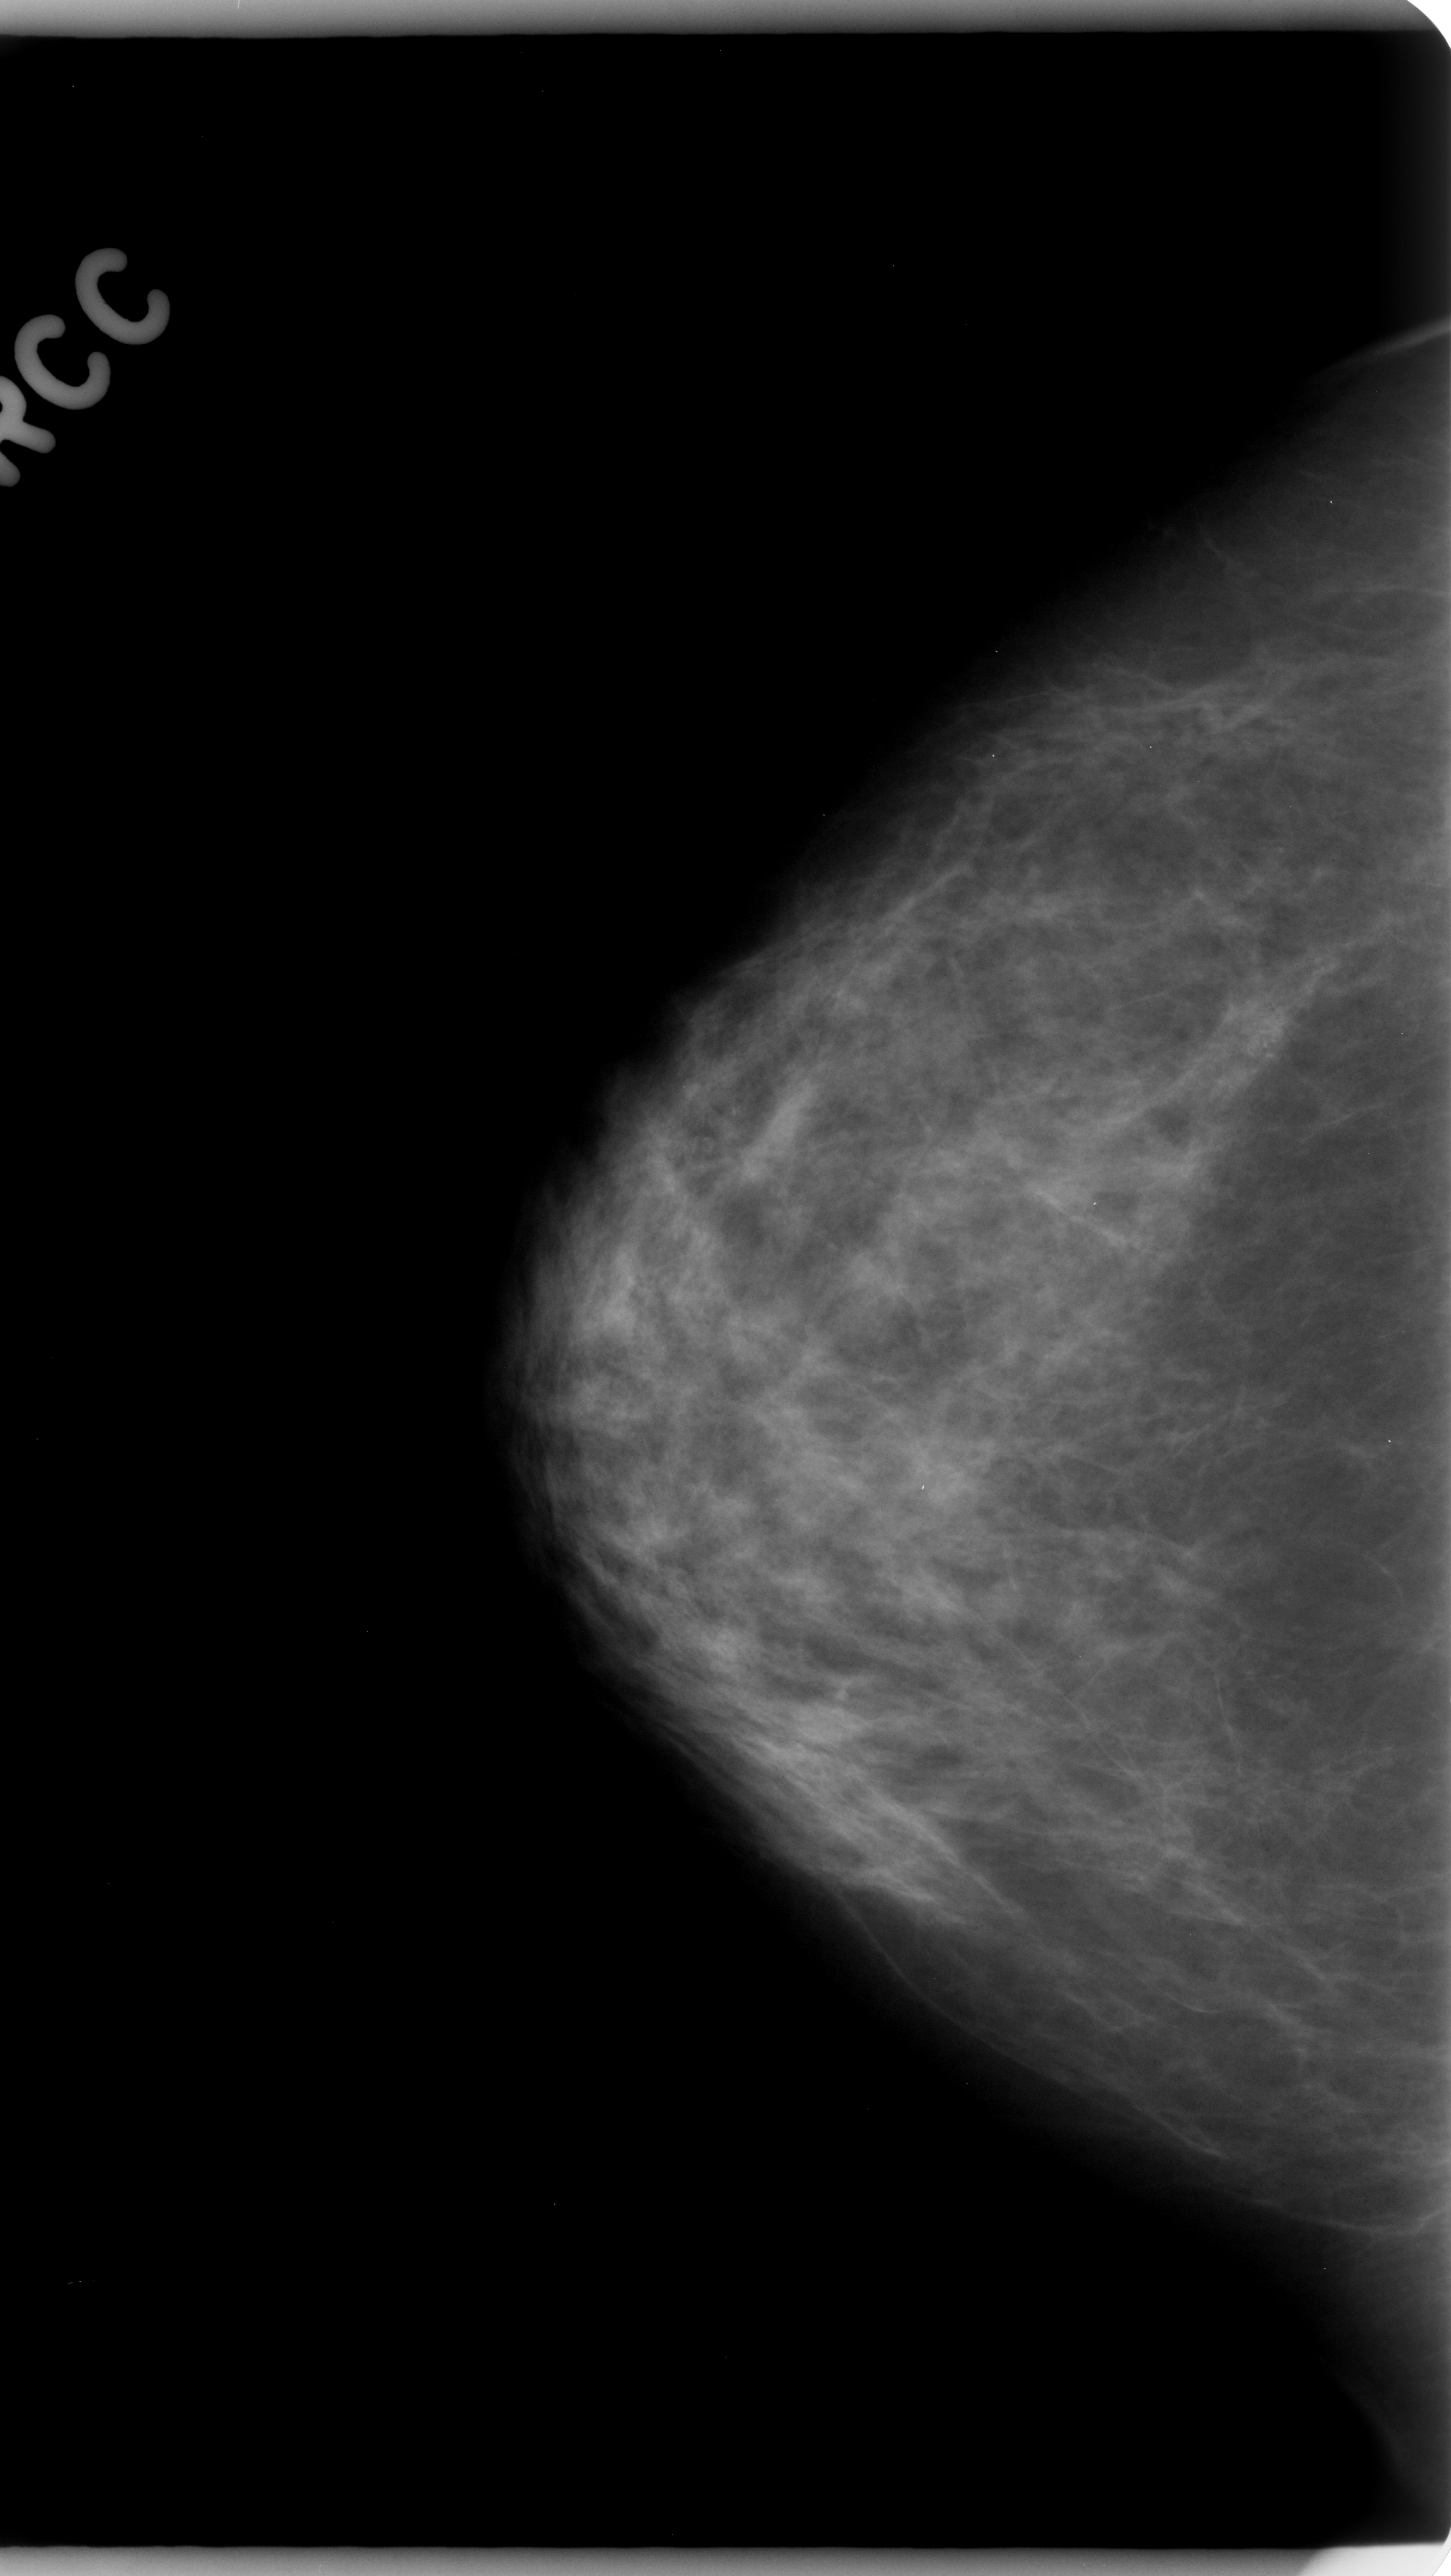
Digitized screen-film mammogram, right breast, CC view, BI-RADS breast density category 2 (scale 1–4).
- Marked findings (only marked abnormalities are described; nothing is implied about the rest of the image): calcifications, morphology pleomorphic, distribution clustered; BI-RADS assessment category 4; subtlety rating 3 on a 1 (subtle) to 5 (obvious) scale; pathology result (as recorded, not read from the image): malignant.